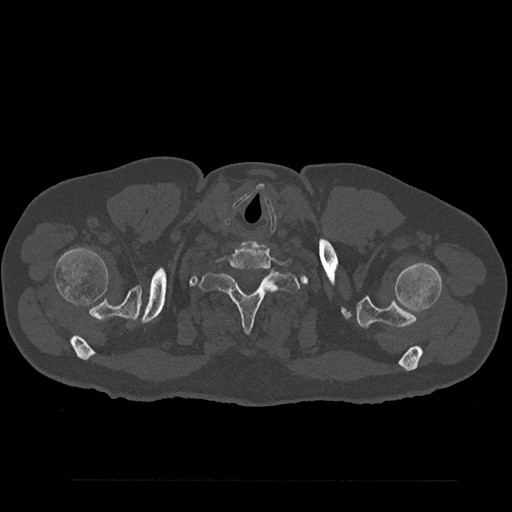
CT including the spine, one axial slice. Position 760 of 797 along the scan axis. Bone window (W 1800 / L 400 HU). 0.5 mm slice thickness. 512 × 512 image matrix, field of view 430 × 430 mm. Male patient, age 61 years. From the clinical record (not read from this slice): primary cancer: prostate.
Outlined on this slice (semi-automatically segmented with operator editing):
- T1 vertebra: bounding box (x1, y1, x2, y2) in pixels: (199, 261, 300, 333)